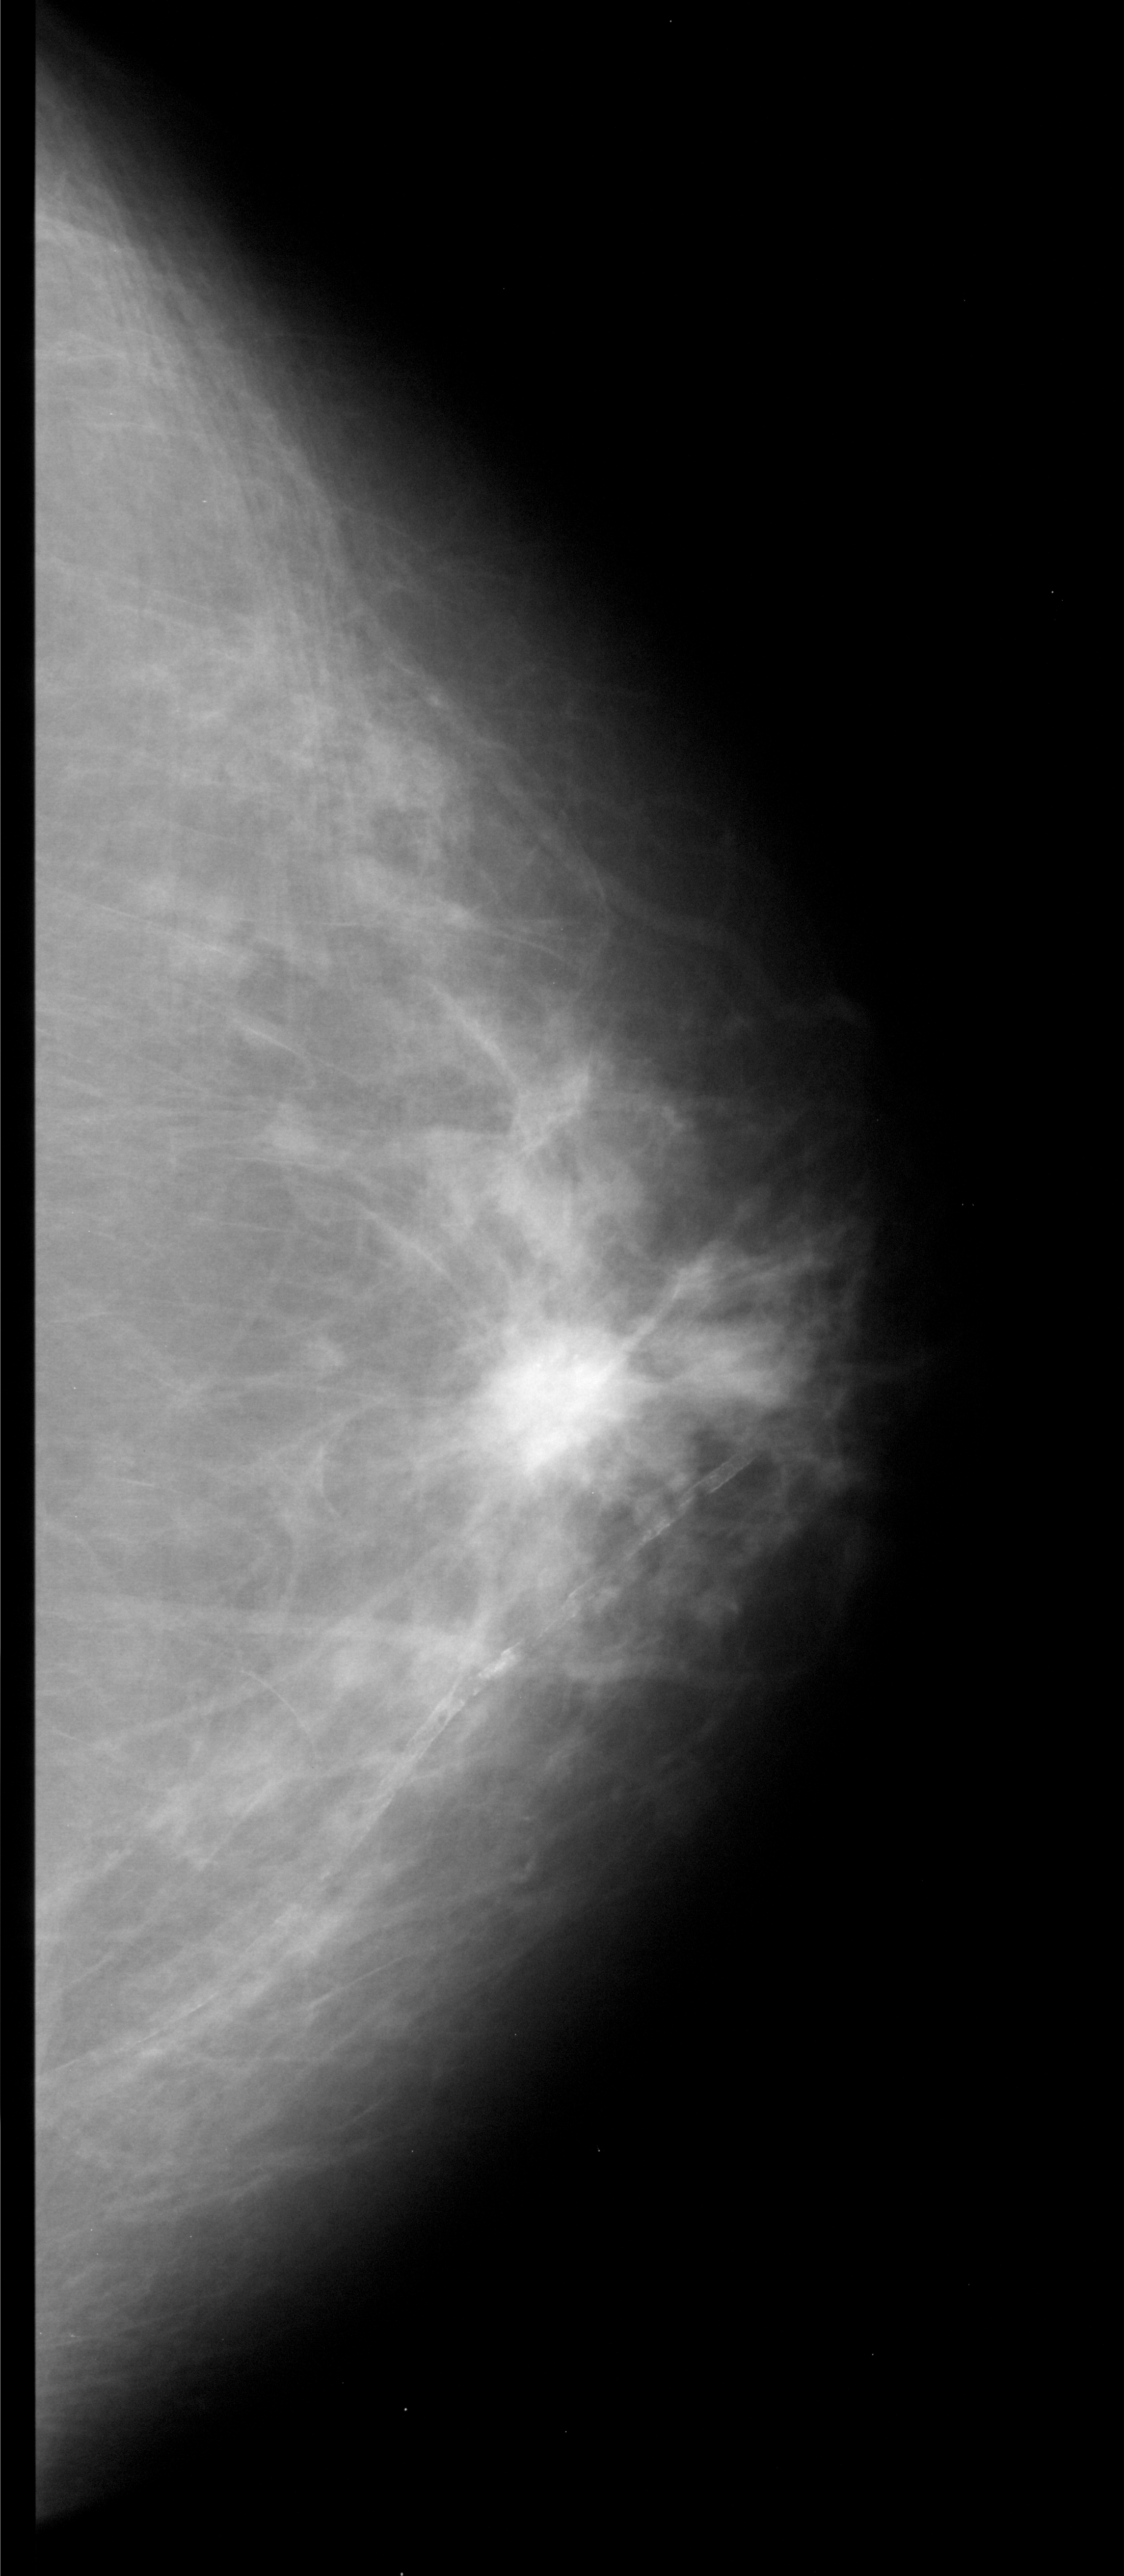
Scanned film-screen mammogram; right breast; CC view; breast composition: scattered fibroglandular densities (BI-RADS density category 2 of 4).
- Mass, shape irregular, margins spiculated; BI-RADS assessment category 5; pathology (as recorded): malignant.